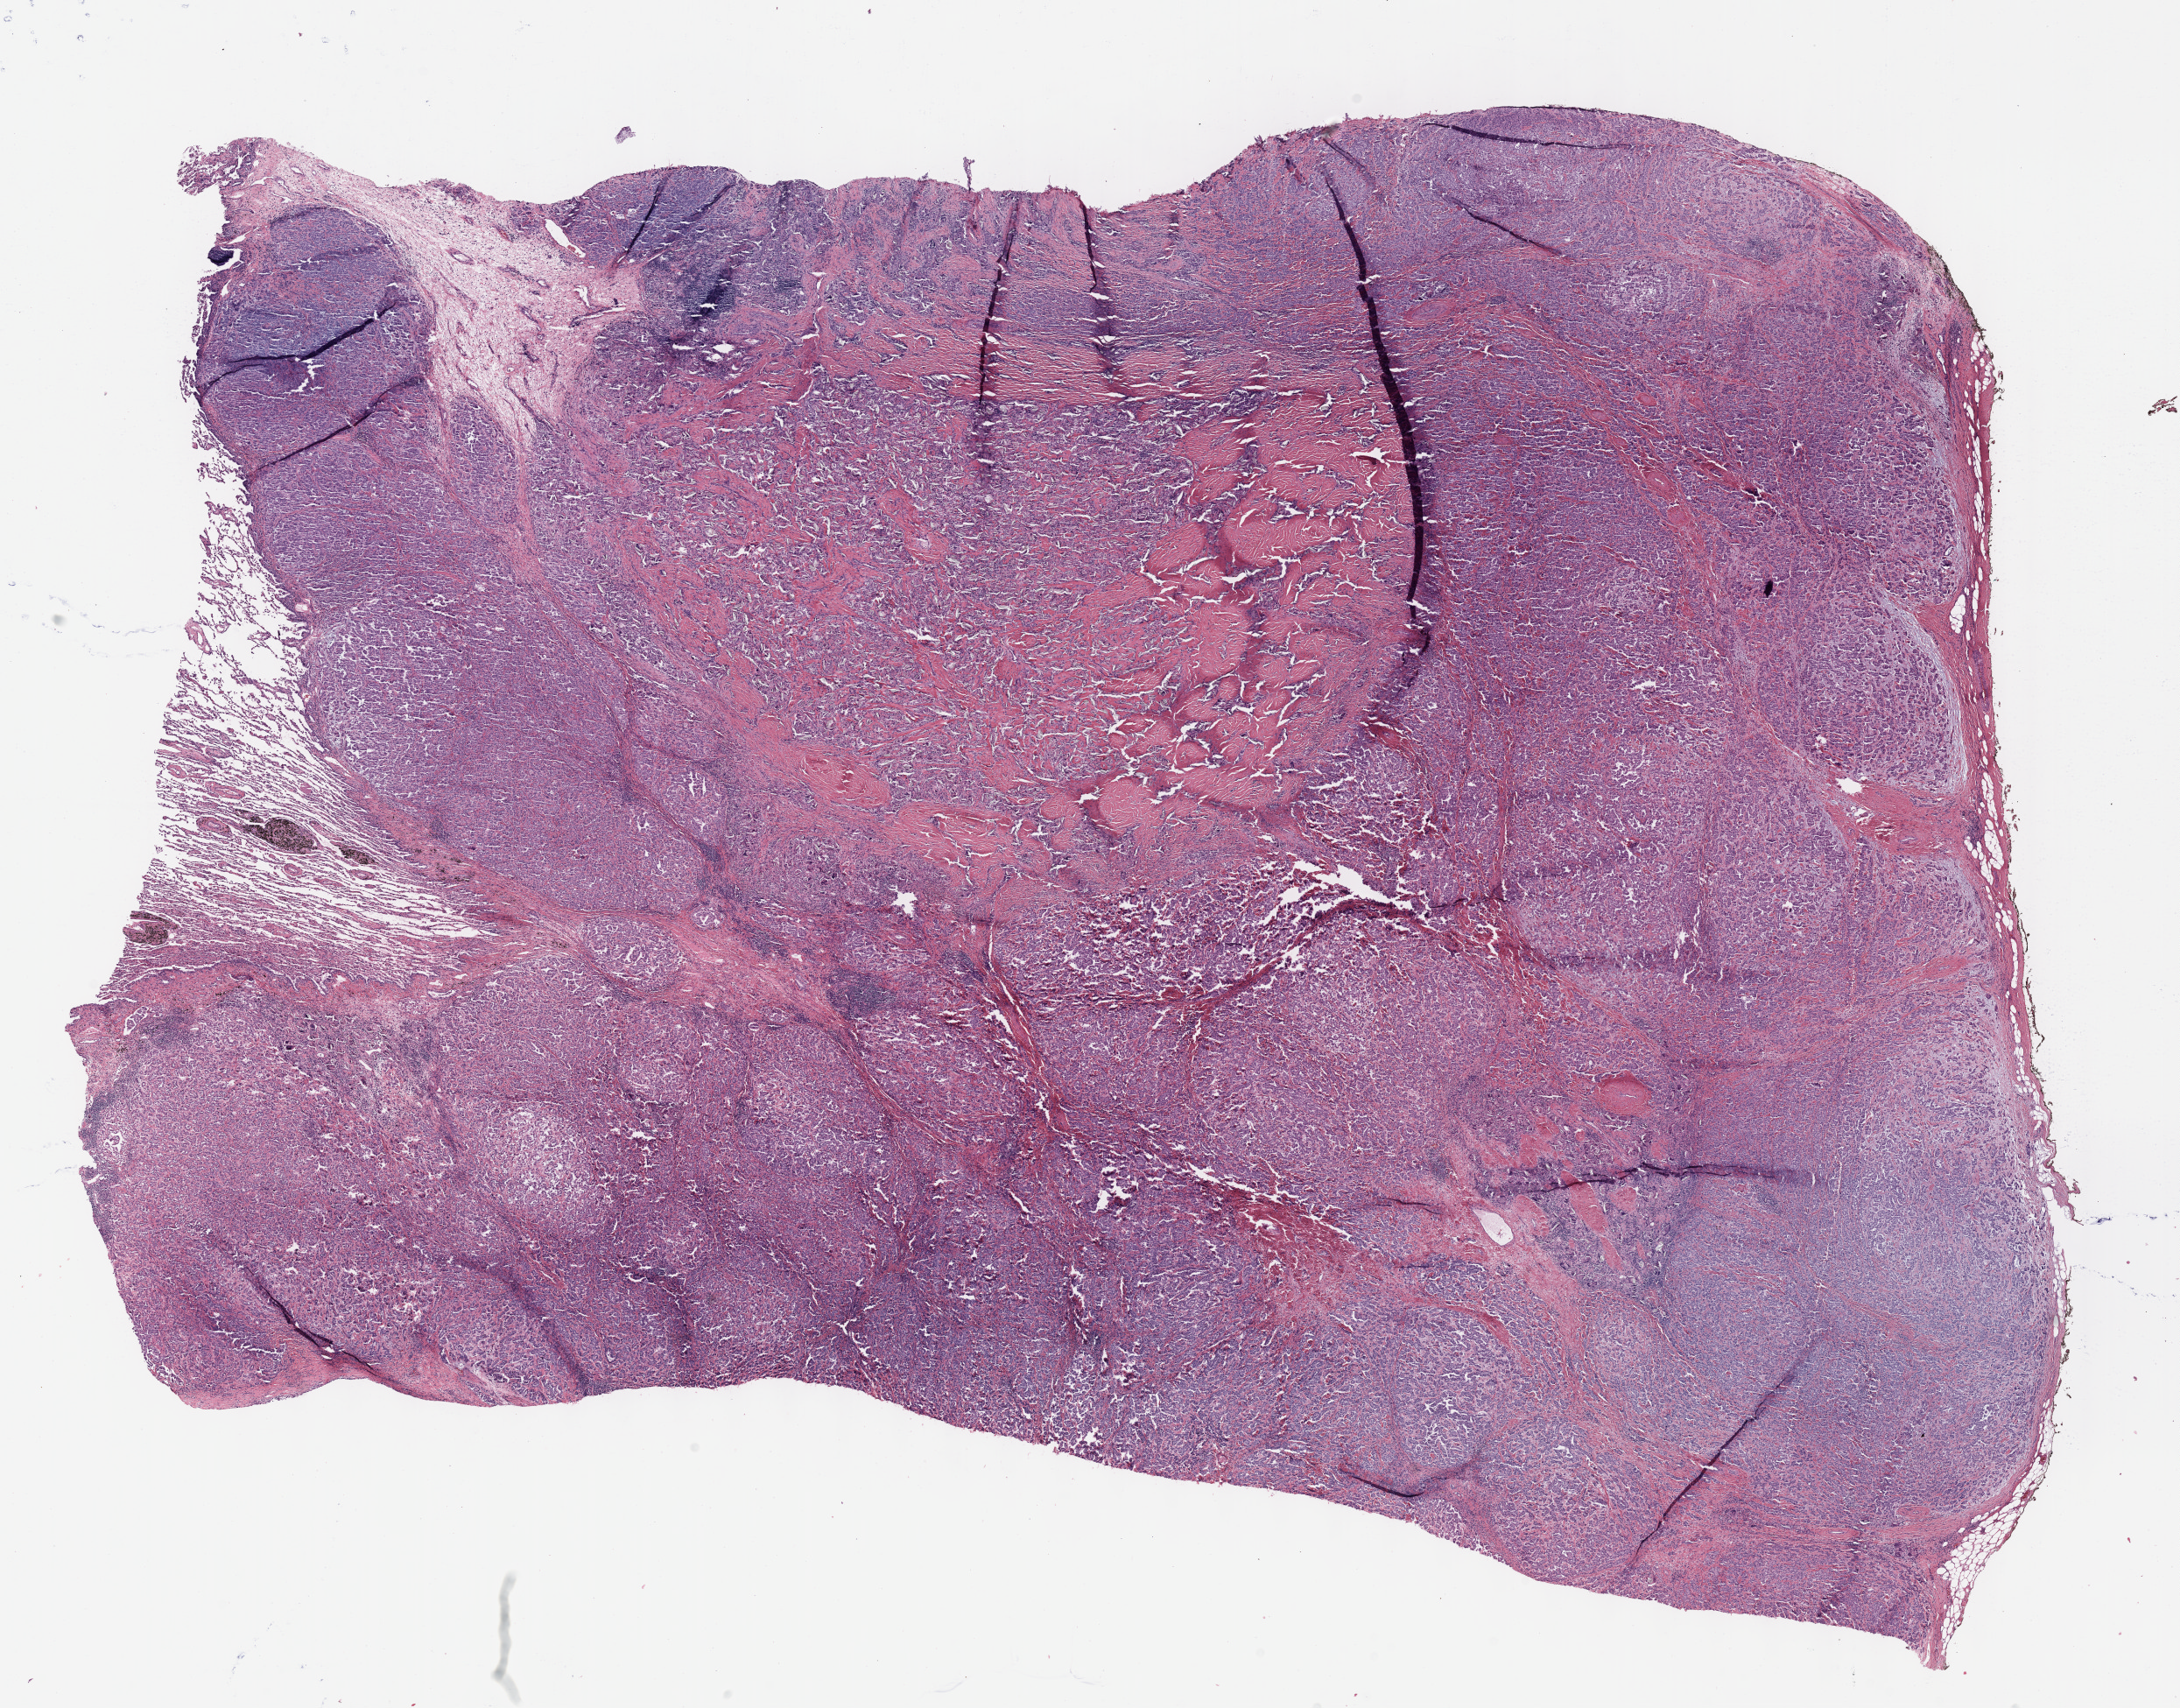
Digitized H&E-stained tissue section (whole slide) — low-resolution overview of the scanned area, about 20.1 x 15.8 mm (slide scanned at 40x). Formalin-fixed paraffin-embedded (FFPE) diagnostic section. Mesothelium, primary tumour sample. Patient: male, age at initial diagnosis 54 years.
Diagnosis: Epithelioid mesothelioma, malignant (pleura, NOS).